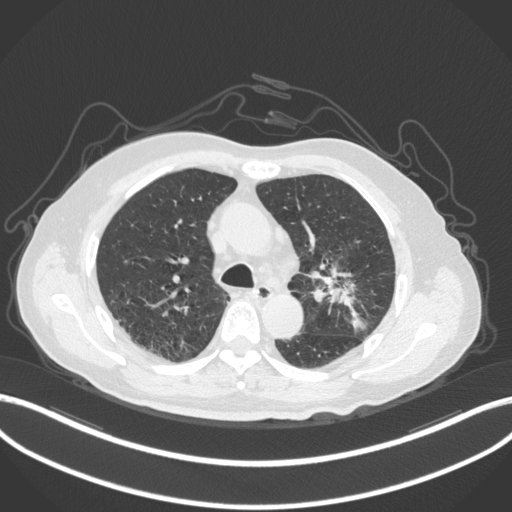
Chest CT, one axial slice; position 192 of 331 along the scan axis; reconstruction kernel B31f; lung window (W 1500 / L -600 HU); 1 mm slice thickness; 512 × 512 image matrix. Patient: male, 79 years. From the clinical record (not read from this slice): clinical TNM (as recorded): T2a N1 M1; histopathological grade: G3.
Structures marked on this image (rectangle marked by the reading radiologist):
- lung tumour (recorded histology: adenocarcinoma): box from (x=322, y=265) to (x=370, y=338) px